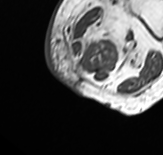
MRI of an extremity soft-tissue mass, one axial slice. Slice 5 of 65 in the series (ordered by position). MR volume resampled by the dataset authors to the PET/CT grid (not the native acquisition matrix). 163 × 155 image matrix, field of view 159 × 151 mm. Female patient. From the clinical record (not read from this slice): histological type: pleomorphic leiomyosarcoma; grade: high; site of the primary tumour: left thigh.
Outlined on this slice (expert contour drawn on MRI and transferred to this co-registered scan by the dataset authors):
- gross tumour volume including surrounding oedema: bounding box (x1, y1, x2, y2) in pixels: (67, 3, 145, 73)